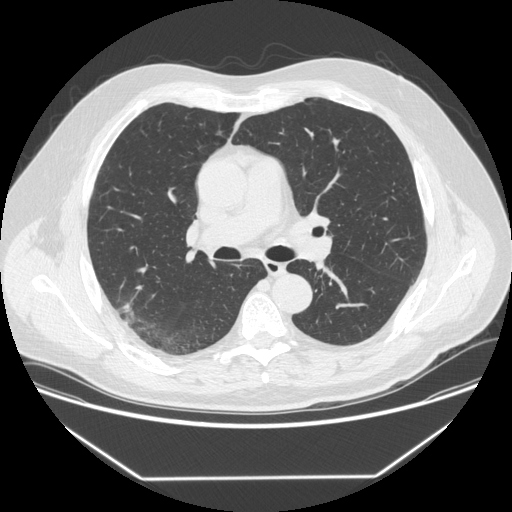
Low-dose screening chest CT, one axial slice; position 216 of 342 along the scan axis; reconstruction kernel STANDARD; lung window (W 1500 / L -600 HU); 512 × 512 image matrix, field of view 410 × 410 mm.
Outlined on this slice (expert manual segmentation):
- lesion 1 (tumor, upper lobe of right lung): bounding box <120,304,134,323> (left, top, right, bottom; pixels)